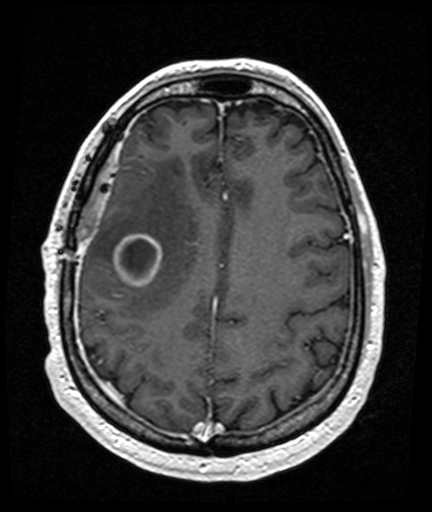
Brain MRI from a brain-tumour surgery series, one axial slice. Position 52 of 176 along the scan axis. T1-weighted post-contrast. 1 mm slice thickness. 432 × 512 image matrix, field of view 194 × 230 mm. From the clinical record (not read from this slice): histopathology: Glioblastoma; WHO grade: 4; IDH mutation: no; tumour location: Right Frontal Temporal, Posterior Sylvian Fissure.
Structures marked on this image (outlined manually by an expert reader):
- tumour: bounding box [x1, y1, x2, y2] px = [116, 234, 161, 286]